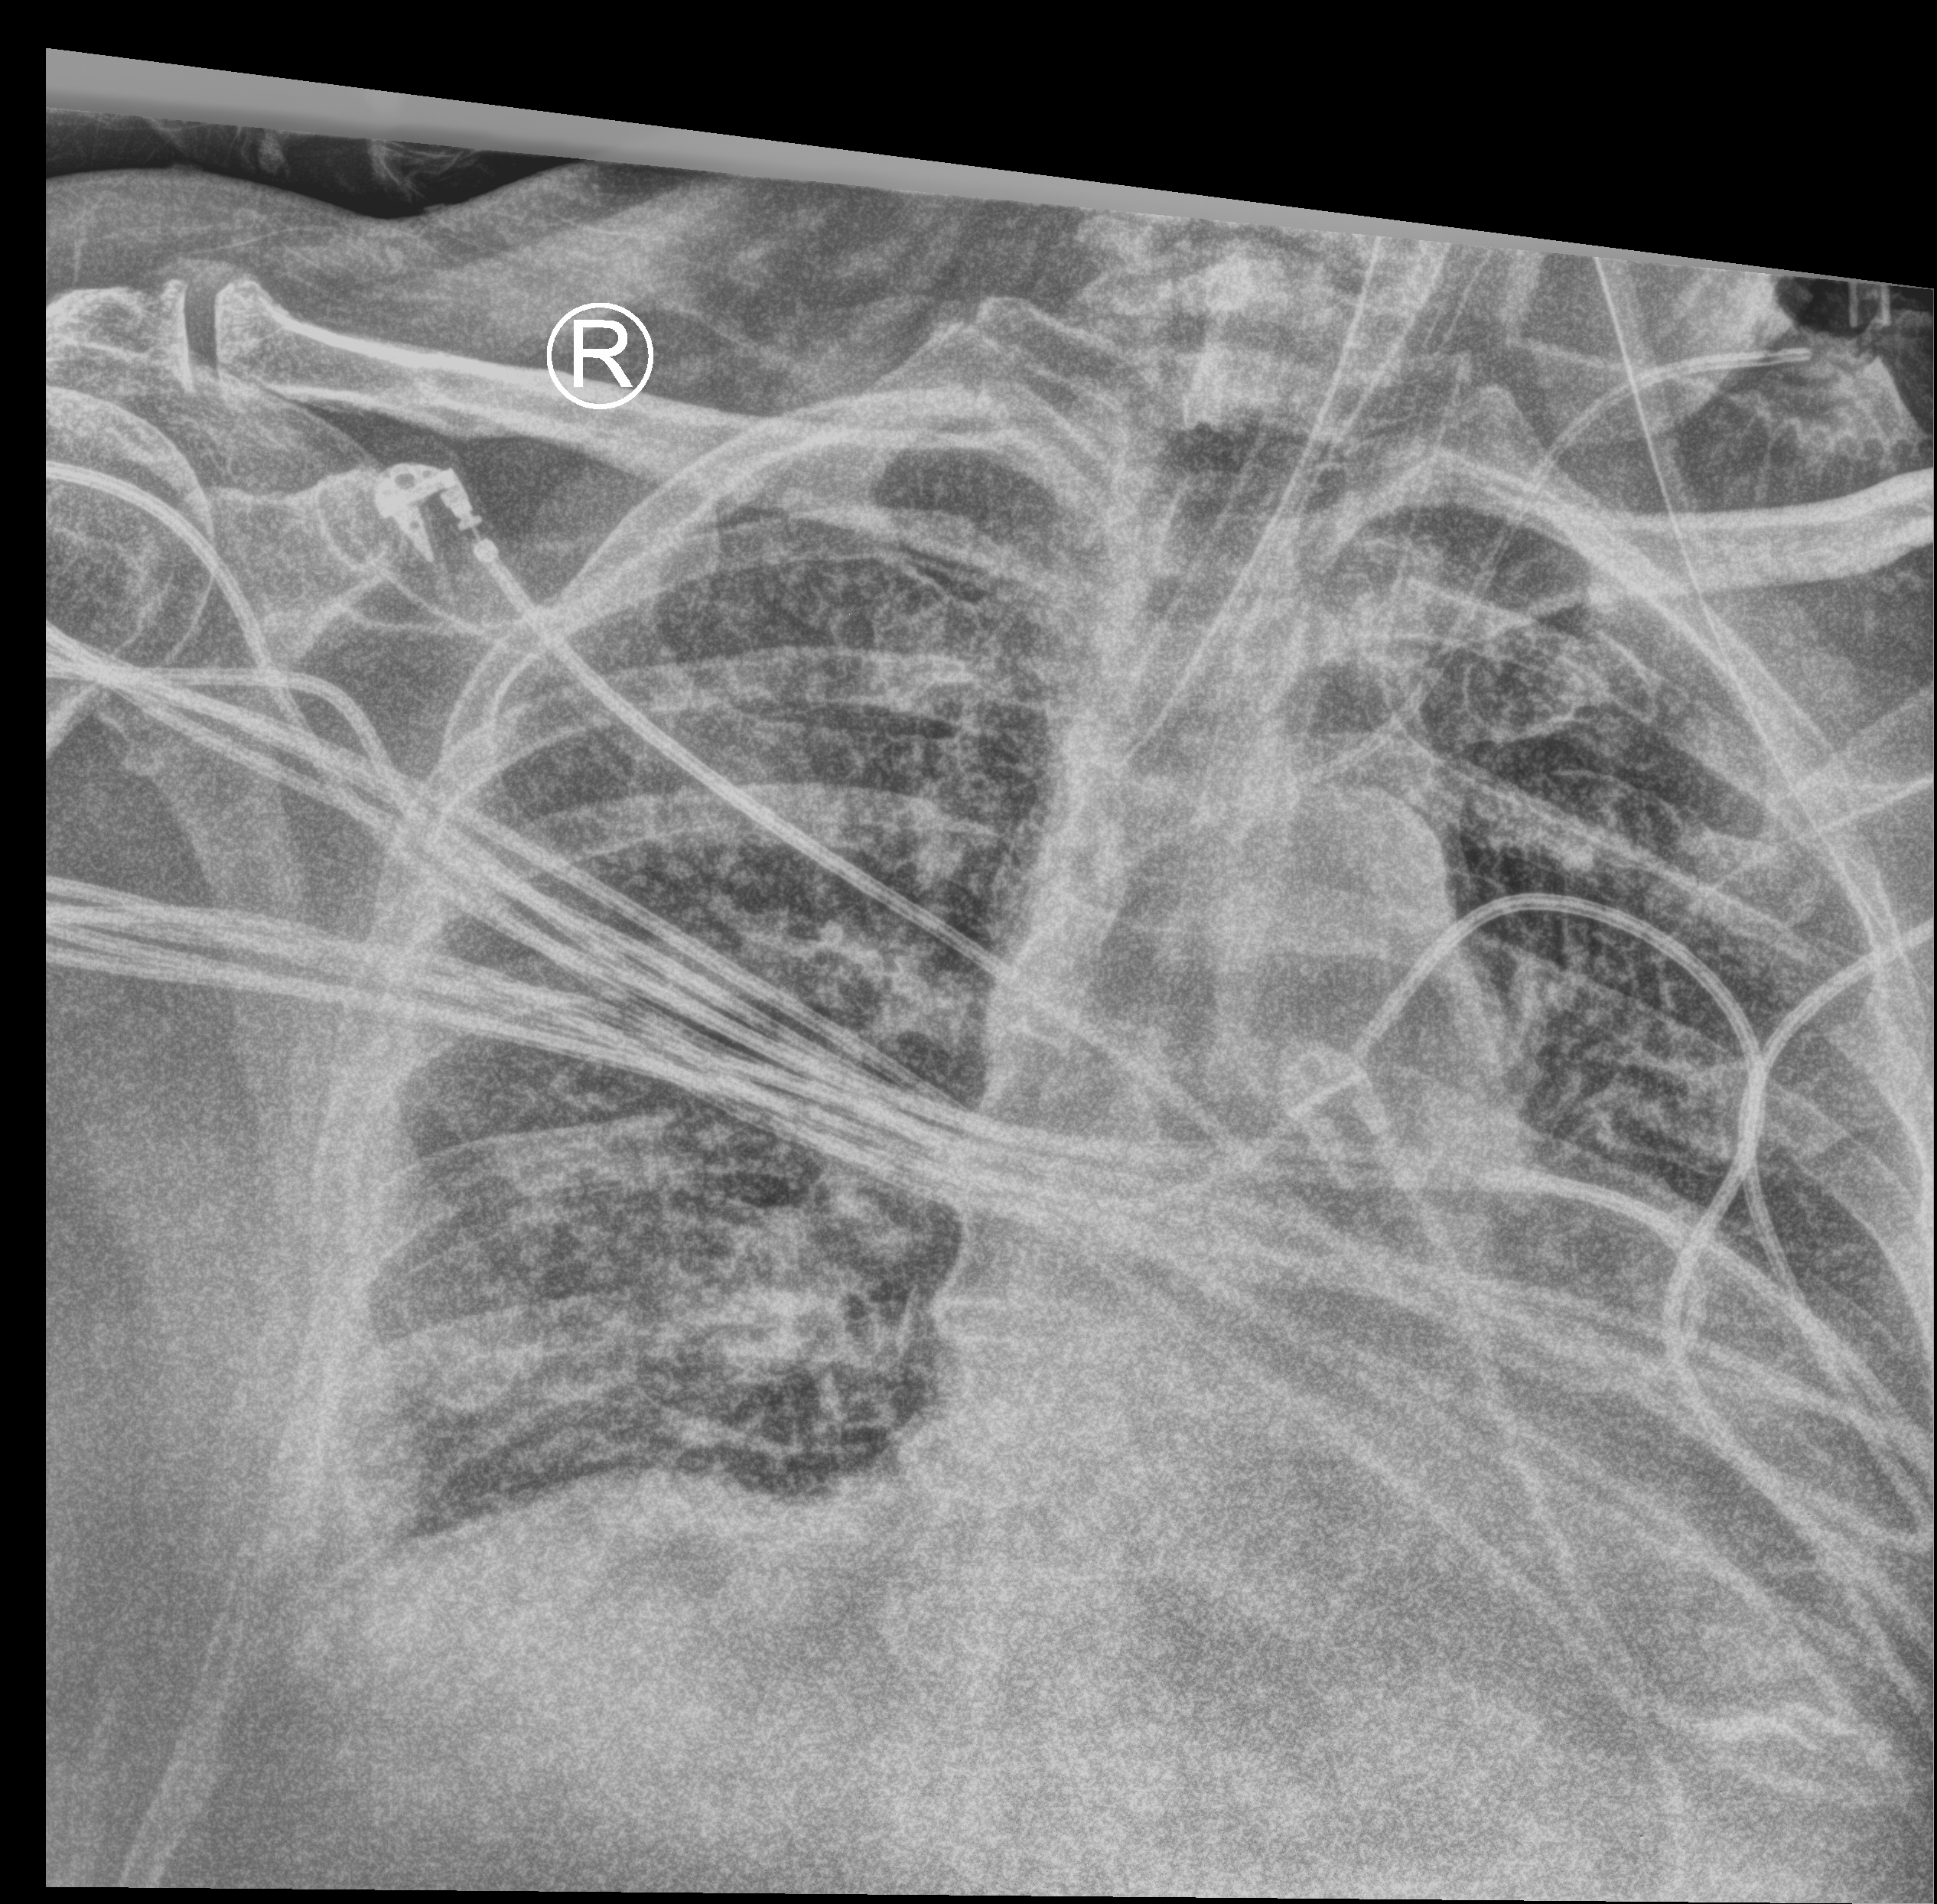
Portable chest radiograph; anteroposterior (AP) projection. Patient hospitalised with COVID-19; male, aged 75–90 years.
Admission-level facts for this patient (not findings on this image; timing relative to this image not recorded): chronic kidney disease (admission record): no.